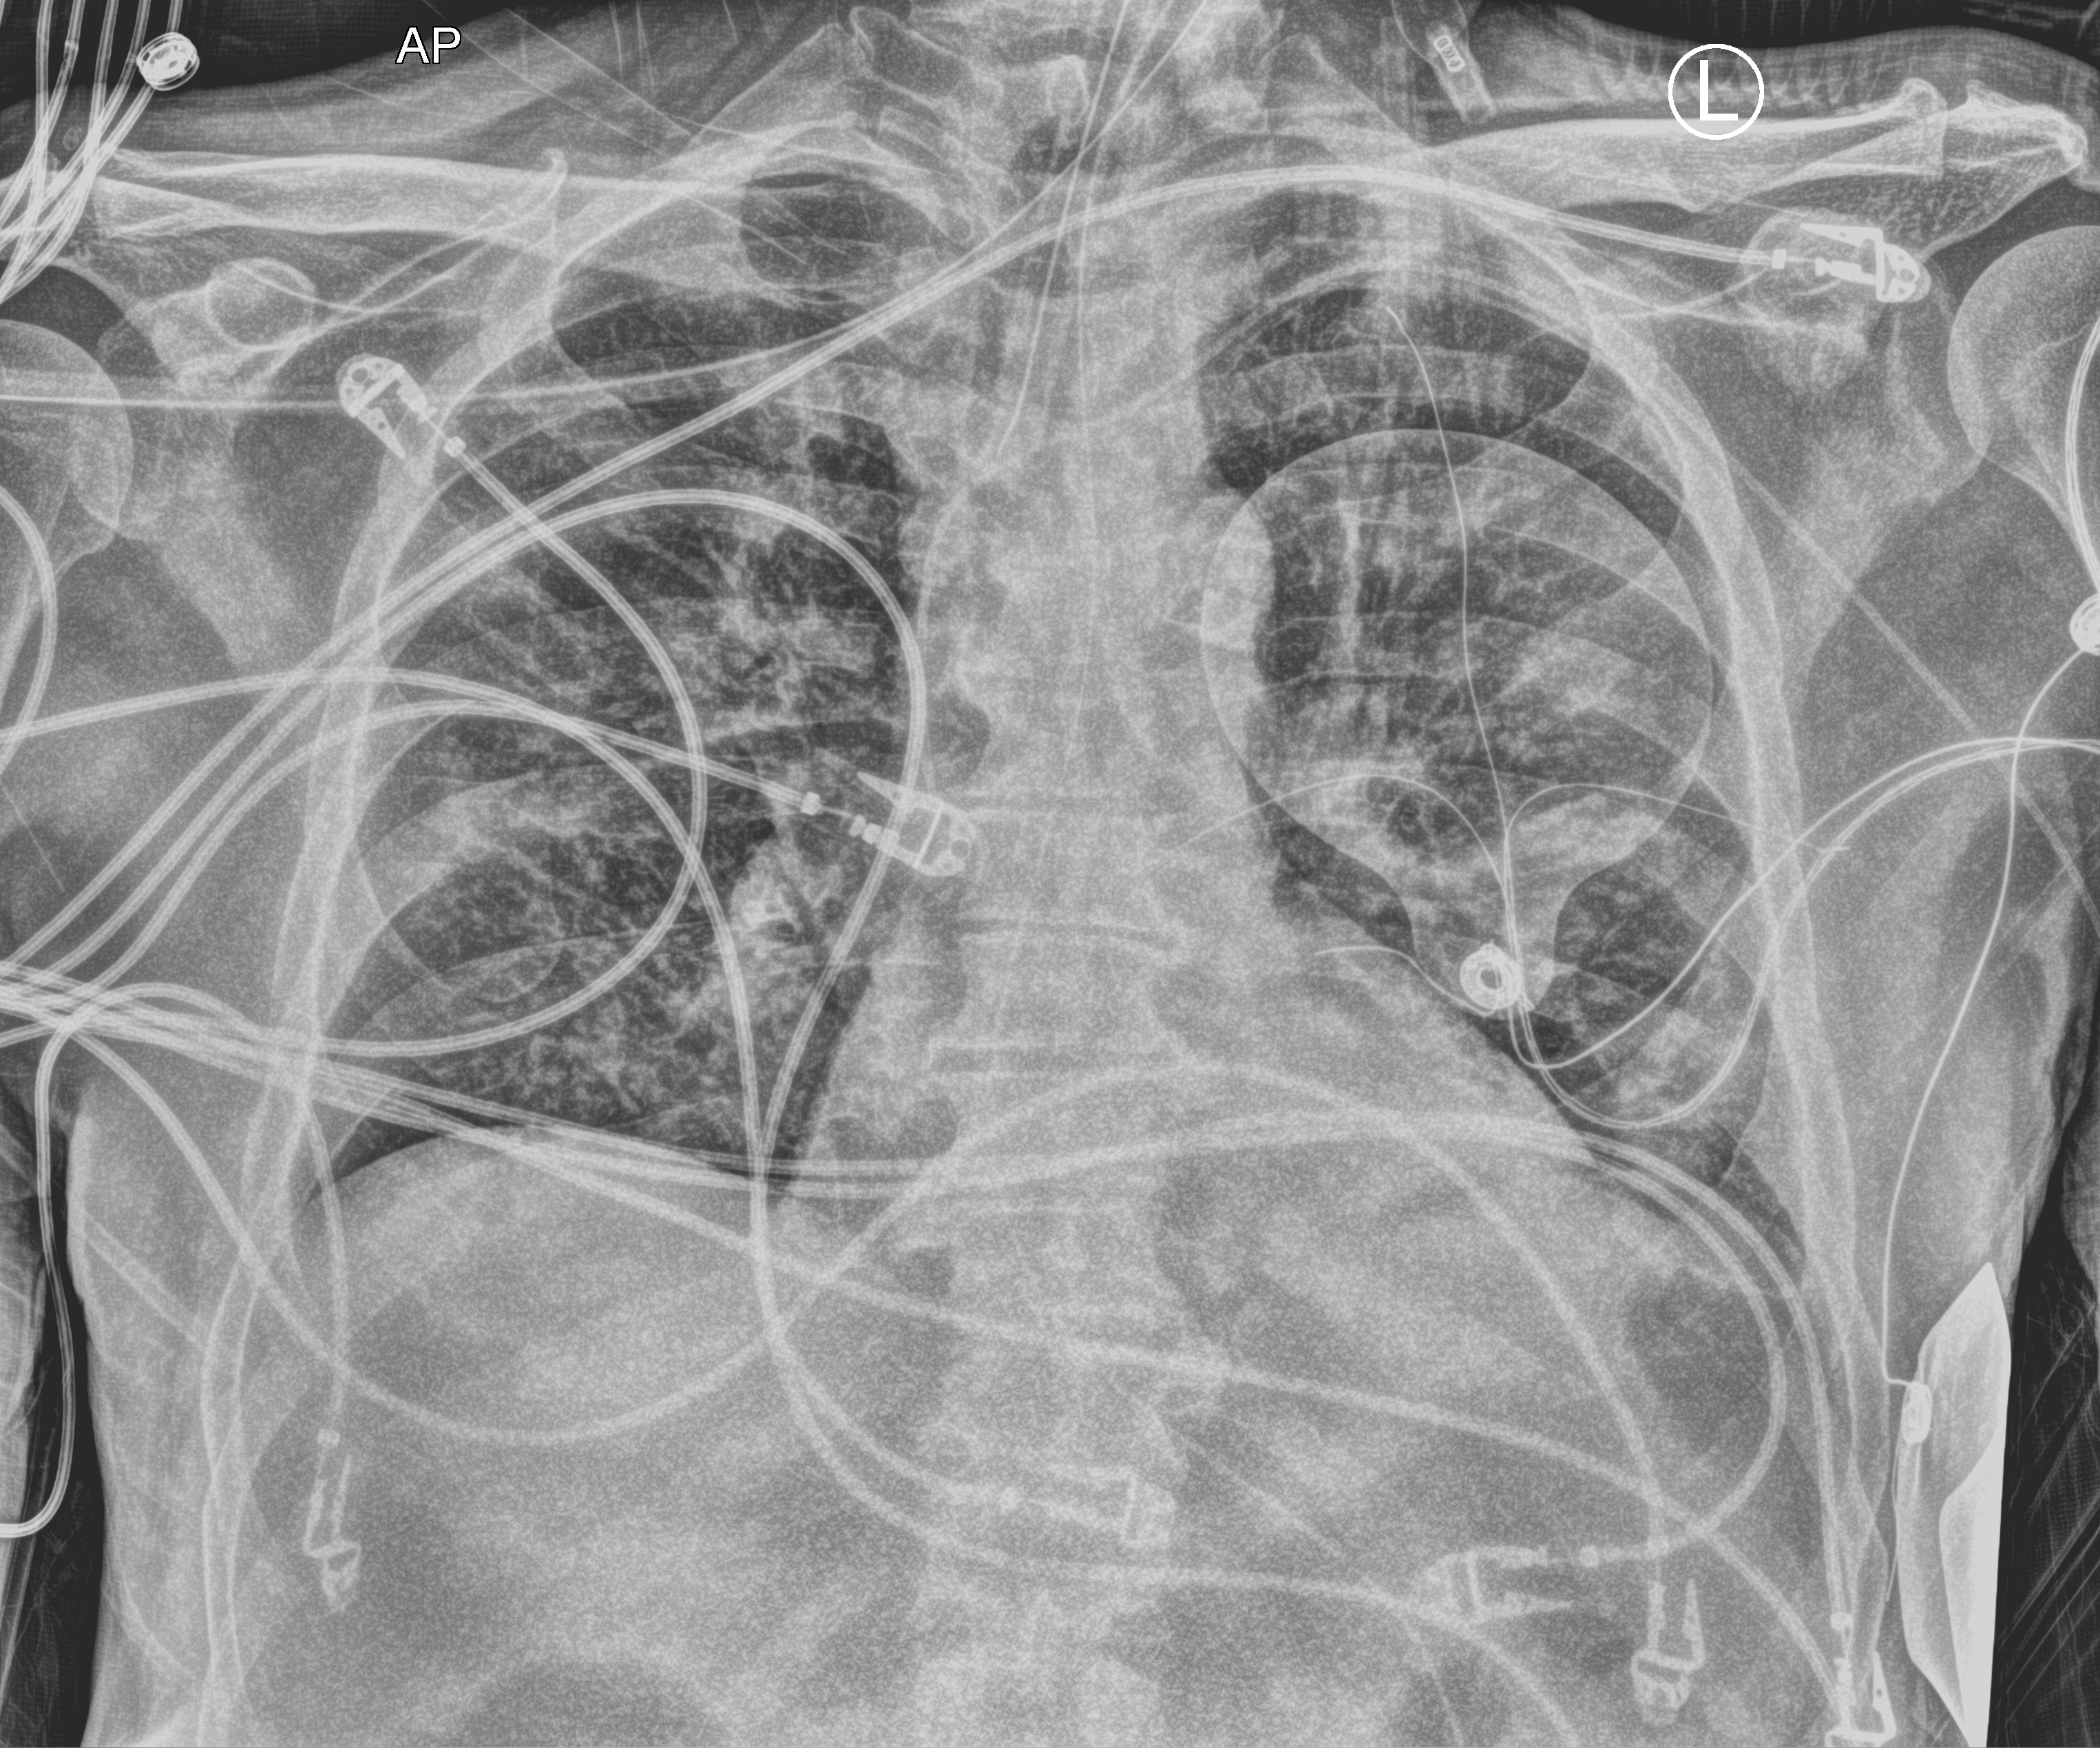
Chest X-ray (portable), anteroposterior (AP) projection. Patient hospitalised with COVID-19; male, aged 60–74 years.
From the hospital-stay record, not from the radiograph (when in the stay this image was taken is not recorded):
- other chronic lung disease (admission record): no
- length of hospital stay: 35 days
- admitted to intensive care during this hospital stay: yes